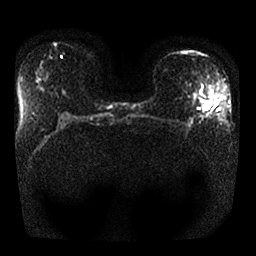
Breast MRI, one axial slice; position 14 of 25 along the scan axis; diffusion-weighted series; image 2 of 4 stored at this slice position (different b-values; order by instance number); 1.5 T; 4 mm slice thickness; 256 × 256 image matrix. Female patient.
Structures marked on this image (manually delineated by an expert):
- tumour on diffusion-weighted imaging: box from (x=203, y=102) to (x=212, y=110) px